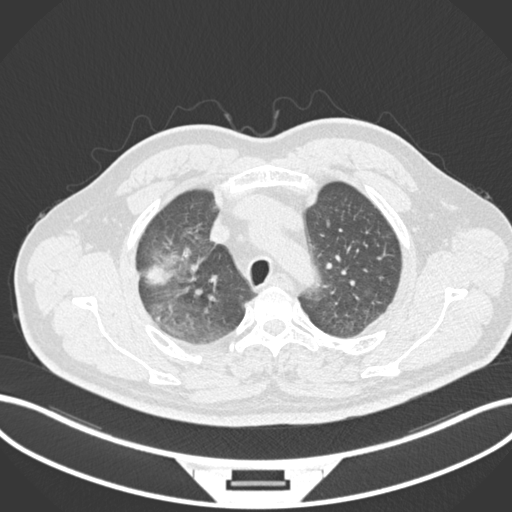
Chest CT, one axial slice. Slice 683 of 852 in the series (ordered by position). 120 kVp. Lung window (W 1500 / L -600 HU). 1 mm slice thickness. 512 × 512 image matrix, field of view 400 × 400 mm. Patient: male, 55 years. From the clinical record (not read from this slice): clinical TNM (as recorded): T3 N2 M1.
Outlined on this slice (rectangle marked by the reading radiologist):
- lung tumour (recorded histology: adenocarcinoma): bounding box <142,250,179,289> (left, top, right, bottom; pixels)